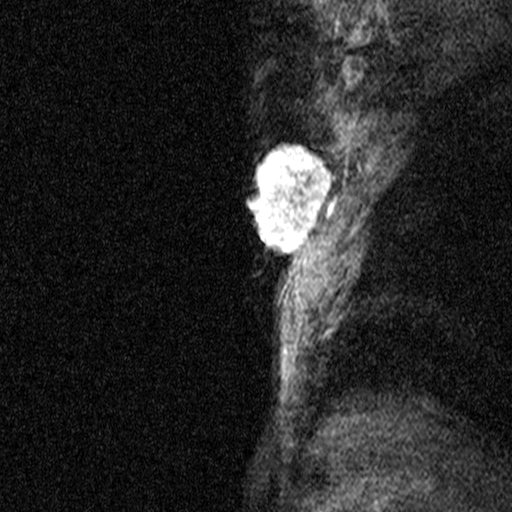
Breast MRI (dynamic contrast-enhanced), one sagittal slice; position 35 of 44 along the scan axis; dynamic contrast-enhanced study with each time point stored as its own series, time point 2 of 3 at this slice position (early post-contrast, ordered by acquisition time); 1.5 T; TE 4.5 ms, TR 11 ms; 3 mm slice thickness; 512 × 512 image matrix, field of view 200 × 200 mm. Female patient, age 44 years. Case-level facts recorded for this patient, not image findings: setting: breast cancer imaged before/during neoadjuvant chemotherapy; receptor status: HR-positive, HER2-negative.
Outlined on this slice (semi-automatically segmented with operator editing):
- analysis volume of interest (the breast-tissue region the enhancement analysis was run in; not a lesion): bounding box [x1, y1, x2, y2] px = [218, 118, 338, 291]
- tumour enhancement mask (voxels above the 90 % enhancement threshold inside the analysis volume of interest): [246, 143, 335, 256]